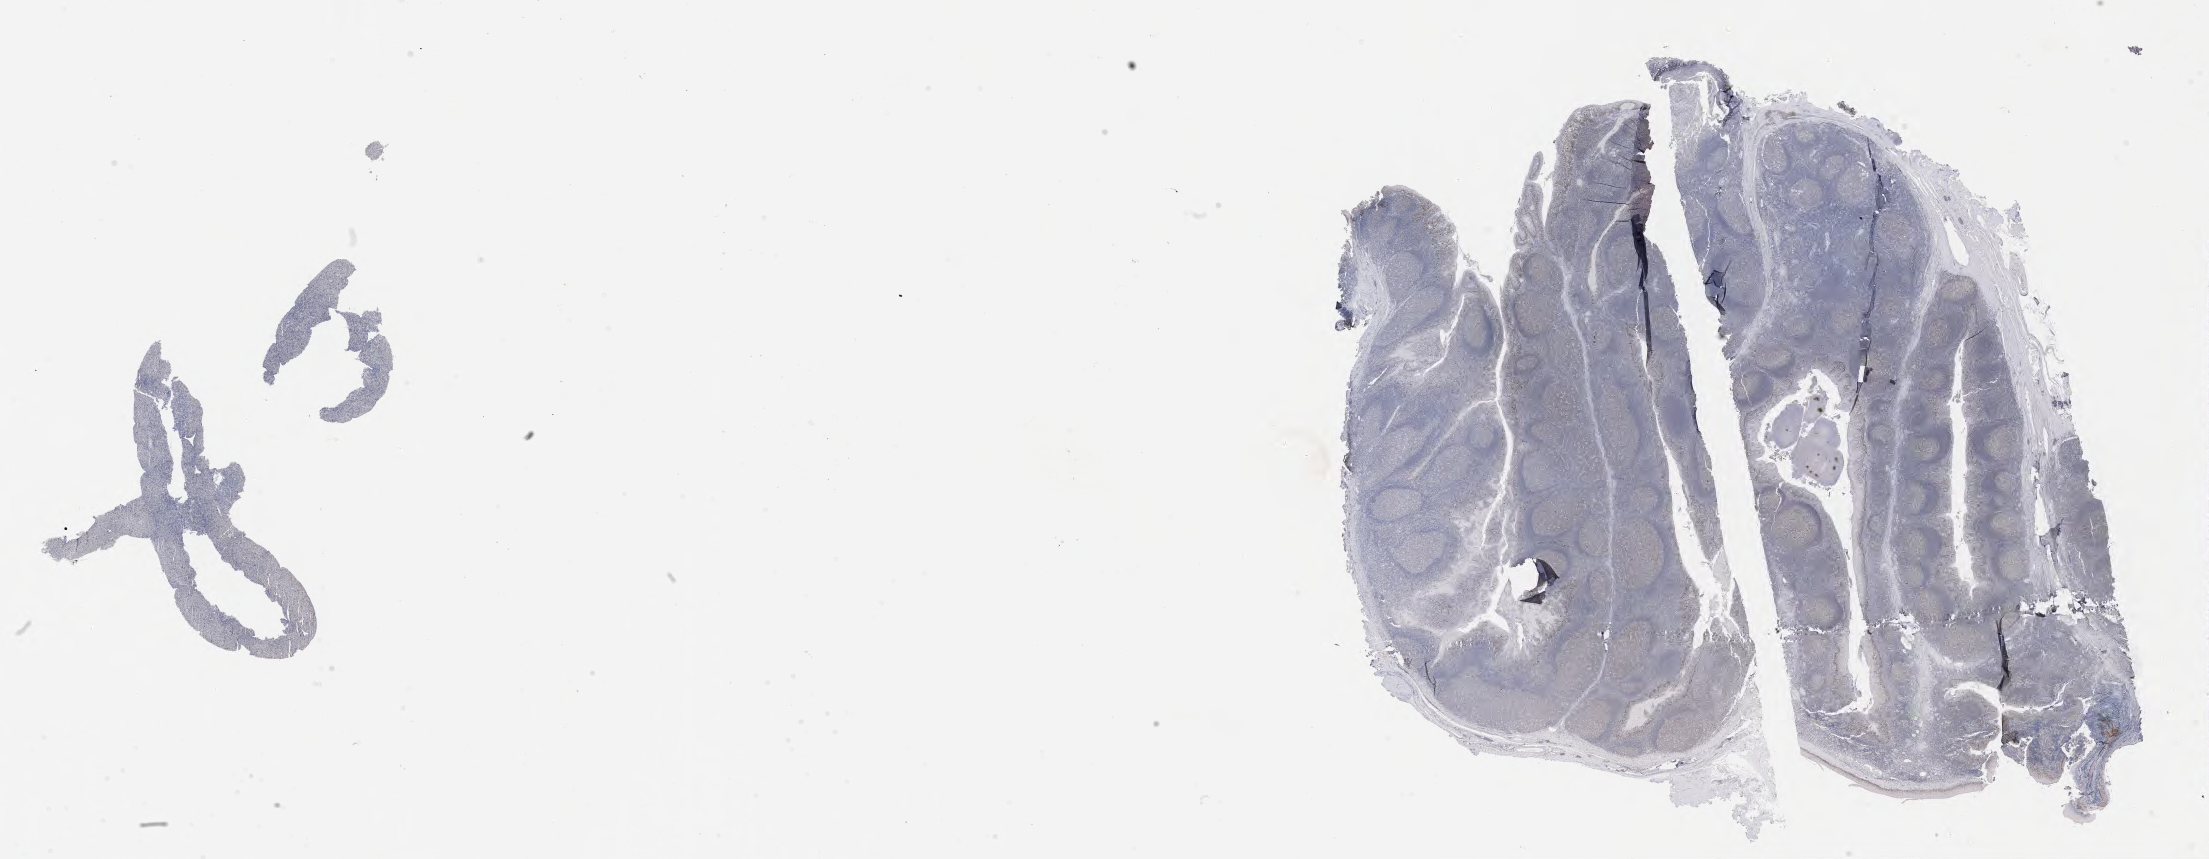
Immunohistochemistry (IHC) whole-slide image stained for p53, a low-resolution overview of the entire scanned area, about 35.7 x 13.9 mm. Male patient, aged 52.
Specimen: tumor tissue; site: liver.